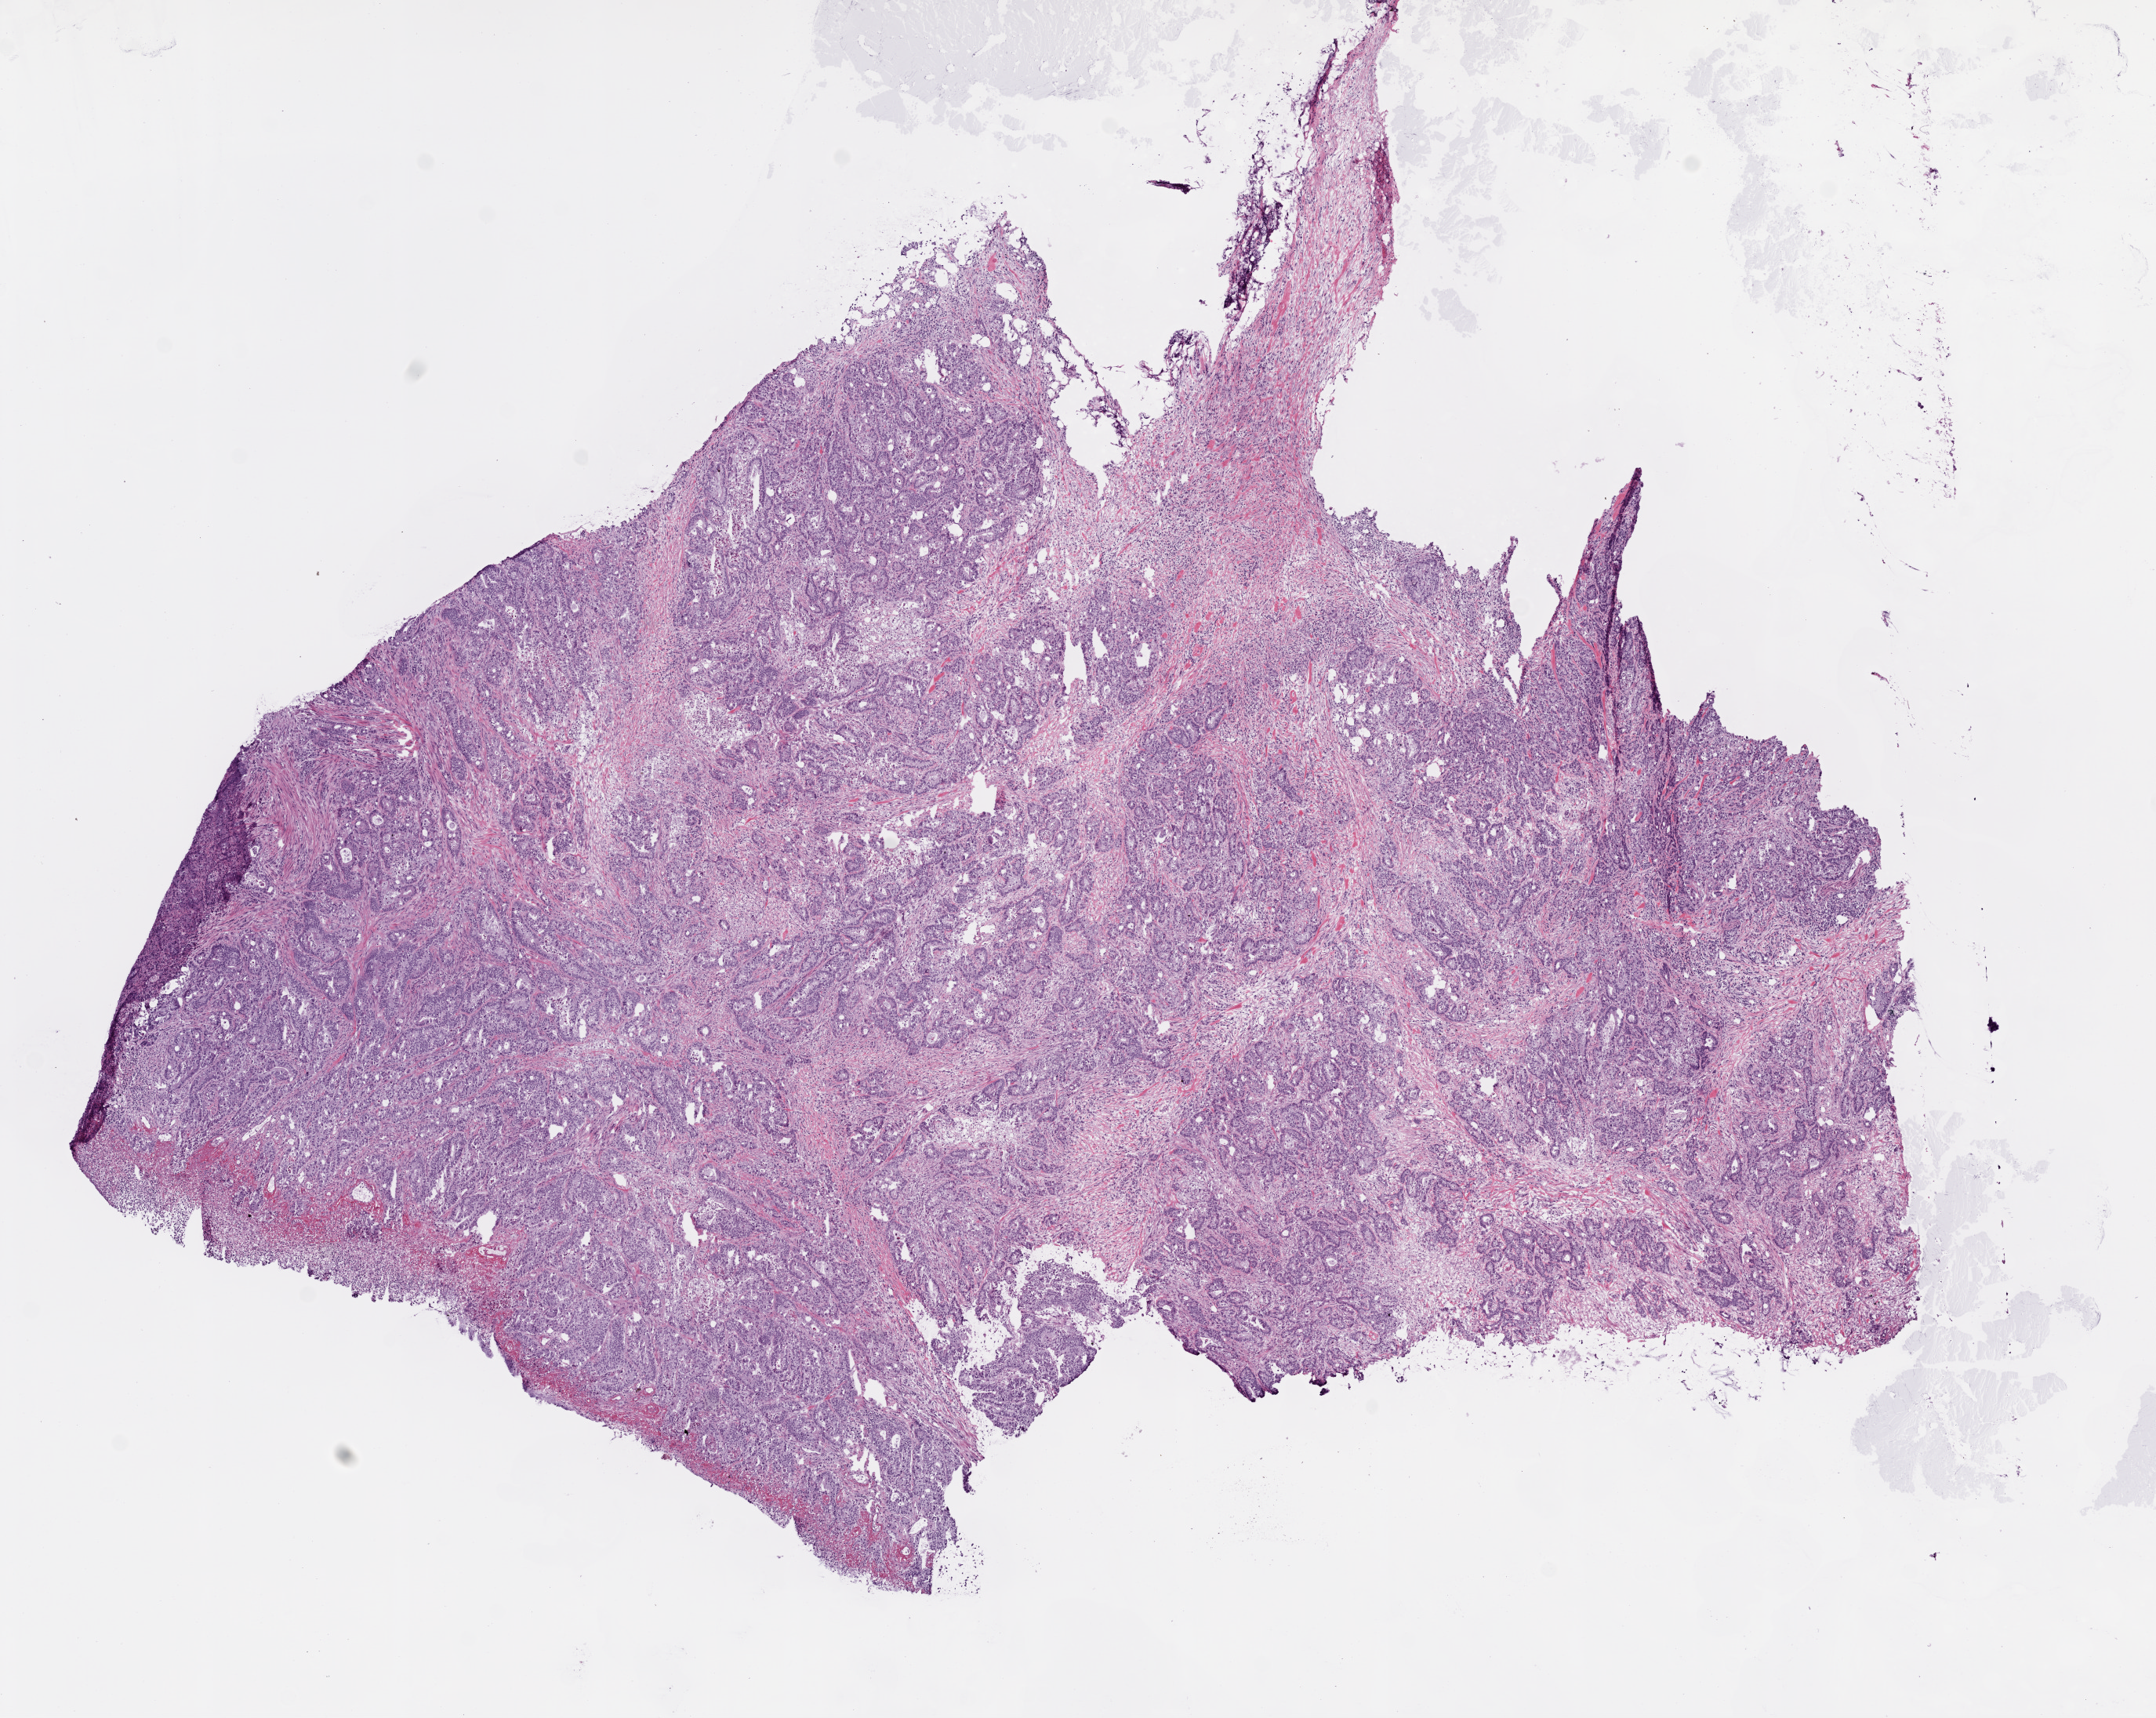
Hematoxylin and eosin (H&E) stained whole-slide image — a low-resolution overview of the entire scanned area, about 11.0 x 8.8 mm, frozen section from the top of the tissue portion, sample: primary tumour, colon. Female, age 60 years at initial diagnosis. Slide review estimates, as recorded: tumour cells 95%, tumour nuclei 80%, normal cells 0%, stromal cells 0%, necrosis 5%. Inflammatory infiltration, as recorded: lymphocyte infiltration 10%, monocyte infiltration 1%, neutrophil infiltration 2%.
• pathologic diagnosis: Adenocarcinoma, NOS (cecum)
• lymph nodes positive (case pathology): 3 of 6 examined
• AJCC pathologic stage: IIIB